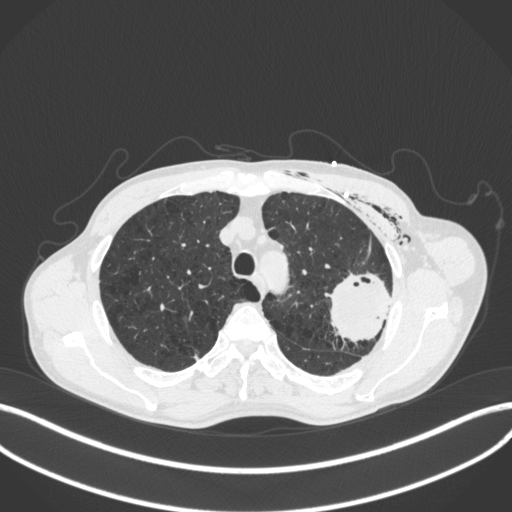
Chest CT, one axial slice. Slice 313 of 416 in the series (ordered by position). Reconstruction kernel B31f. 120 kVp. Lung window (W 1500 / L -600 HU). 1 mm slice thickness. 512 × 512 image matrix, field of view 400 × 400 mm. Patient: male, 58 years. From the clinical record (not read from this slice): clinical TNM (as recorded): T3 N0 M0.
Annotated regions visible in this slice (bounding box drawn by a radiologist):
- lung tumour (recorded histology: adenocarcinoma): box from (x=320, y=270) to (x=401, y=346) px